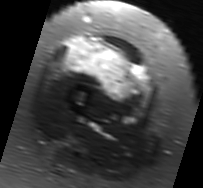
MRI of an extremity soft-tissue mass, one axial slice. T2-weighted fat-saturated. MR volume resampled by the dataset authors to the PET/CT grid (not the native acquisition matrix). 203 × 188 image matrix, field of view 198 × 184 mm. Female patient. From the clinical record (not read from this slice): histological type: malignant solitary fibrous tumor; grade: intermediate; site of the primary tumour: right thigh.
Outlined on this slice (expert contour drawn on MRI and transferred to this co-registered scan by the dataset authors):
- gross tumour volume including surrounding oedema: box from (x=60, y=35) to (x=153, y=105) px
- gross tumour volume (mass): (x=69, y=49)–(x=130, y=93)